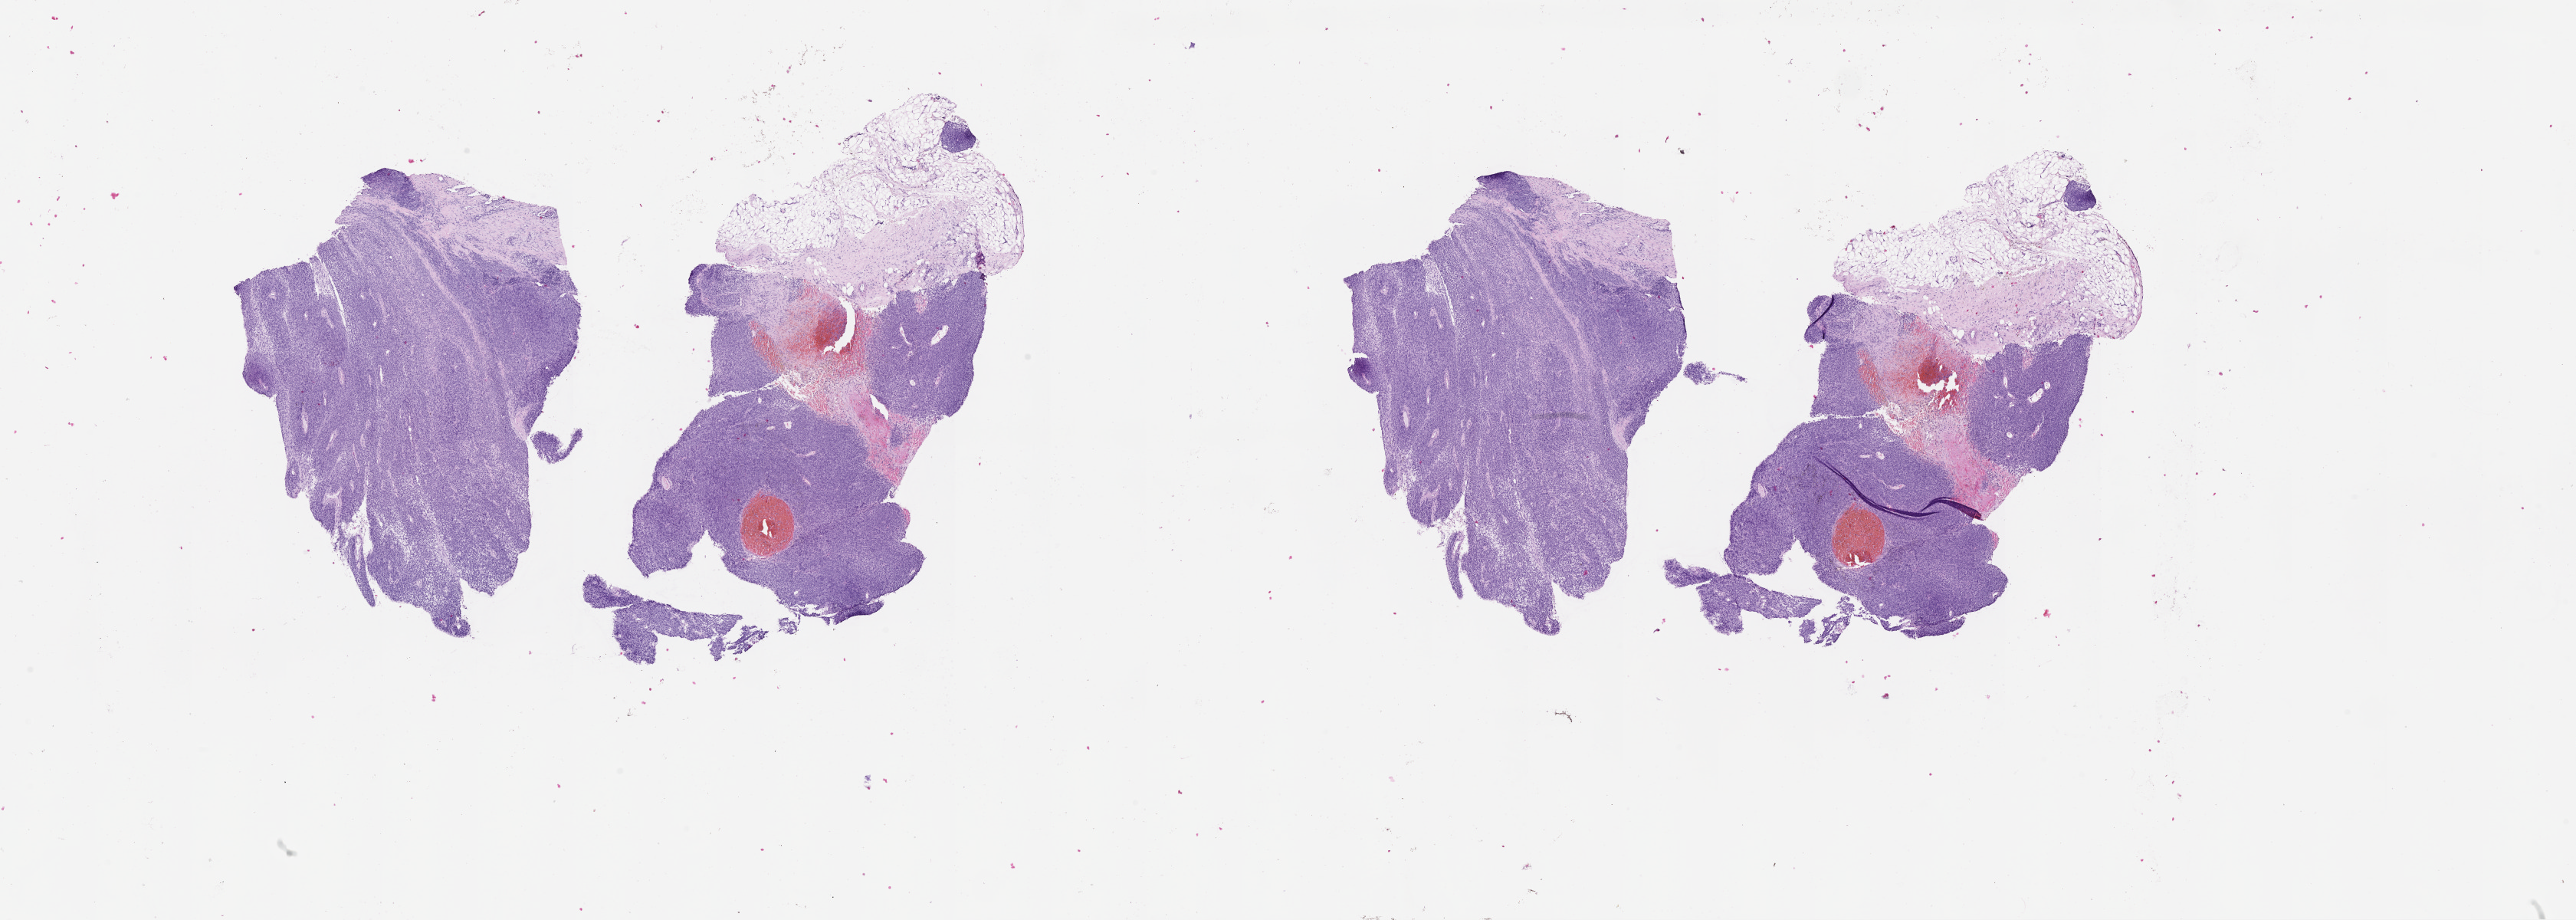
Whole-slide histology image, H&E — whole scanned area (about 27.1 x 9.7 mm) shown as a low-resolution overview. Patient: male, age 72 years.
Patient diagnosis: Malignant melanoma, NOS.